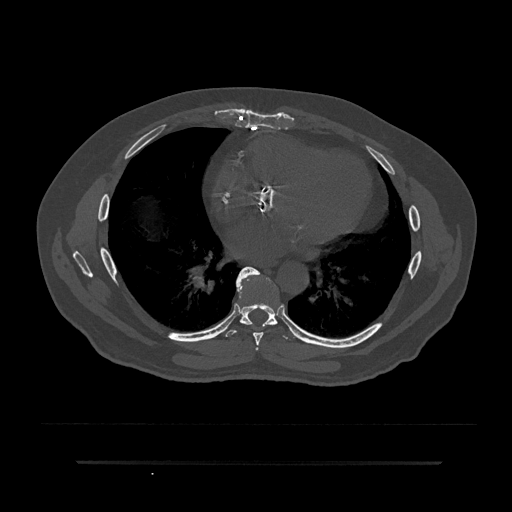
CT including the spine, one axial slice. Position 453 of 797 along the scan axis. Reconstruction kernel Br40s/3. 120 kVp. Bone window (W 1800 / L 400 HU). 0.5 mm slice thickness. 512 × 512 image matrix, field of view 464 × 464 mm. Male patient, age 59 years. From the clinical record (not read from this slice): primary cancer: bile ducts.
Outlined on this slice (semi-automatic segmentation, software-assisted and operator-edited):
- T6 vertebra: bounding box [x1, y1, x2, y2] px = [256, 348, 259, 351]
- T7 vertebra: [236, 266, 268, 346]
- T8 vertebra: [221, 270, 296, 339]